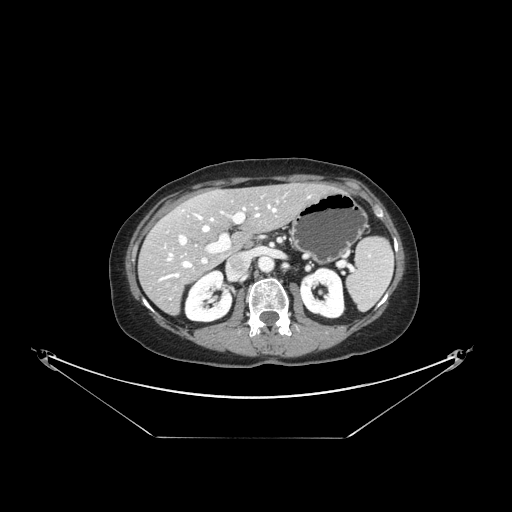
Contrast-enhanced abdominal CT, one axial slice. Slice 83 of 148 in the series (ordered by position). Intravenous contrast given. Soft-tissue window (W 400 / L 40 HU). 2.5 mm slice thickness. 512 × 512 image matrix. Female patient, age 73 years. From the clinical record (not read from this slice): diagnosis: colorectal cancer liver metastases, imaged before liver resection; multiple liver metastases: no; largest metastasis: 1 cm; chemotherapy before resection: yes.
Structures marked on this image (expert manual segmentation):
- hepatic veins: bounding box [x1, y1, x2, y2] px = [160, 205, 277, 280]
- liver: [141, 184, 331, 314]
- planned liver remnant (the part of the liver to remain after resection): [168, 184, 331, 244]
- portal vein (with intrahepatic branches): [179, 207, 258, 264]